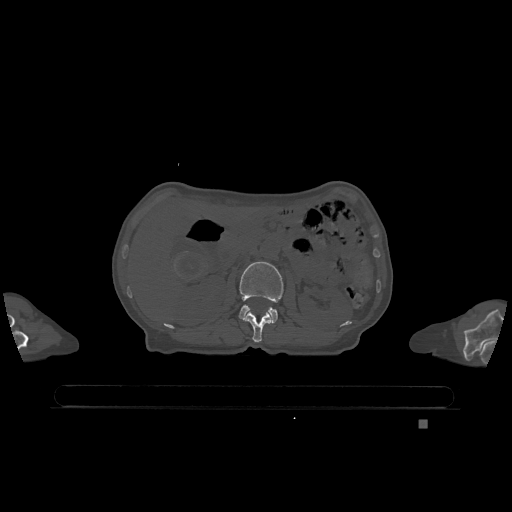
CT including the spine, one axial slice; slice 441 of 1317 in the series (ordered by position); bone window (W 1800 / L 400 HU); 0.5 mm slice thickness; 512 × 512 image matrix, field of view 500 × 500 mm. Patient: female, 74 years. From the clinical record (not read from this slice): primary cancer: lung; vertebrae with lytic lesions (as recorded): T1, T4, T5, T6, L4, L5.
Annotated regions visible in this slice (semi-automatically segmented with operator editing):
- L1 vertebra: bounding box (x1, y1, x2, y2) in pixels: (244, 311, 272, 343)
- L2 vertebra: (239, 262, 284, 323)